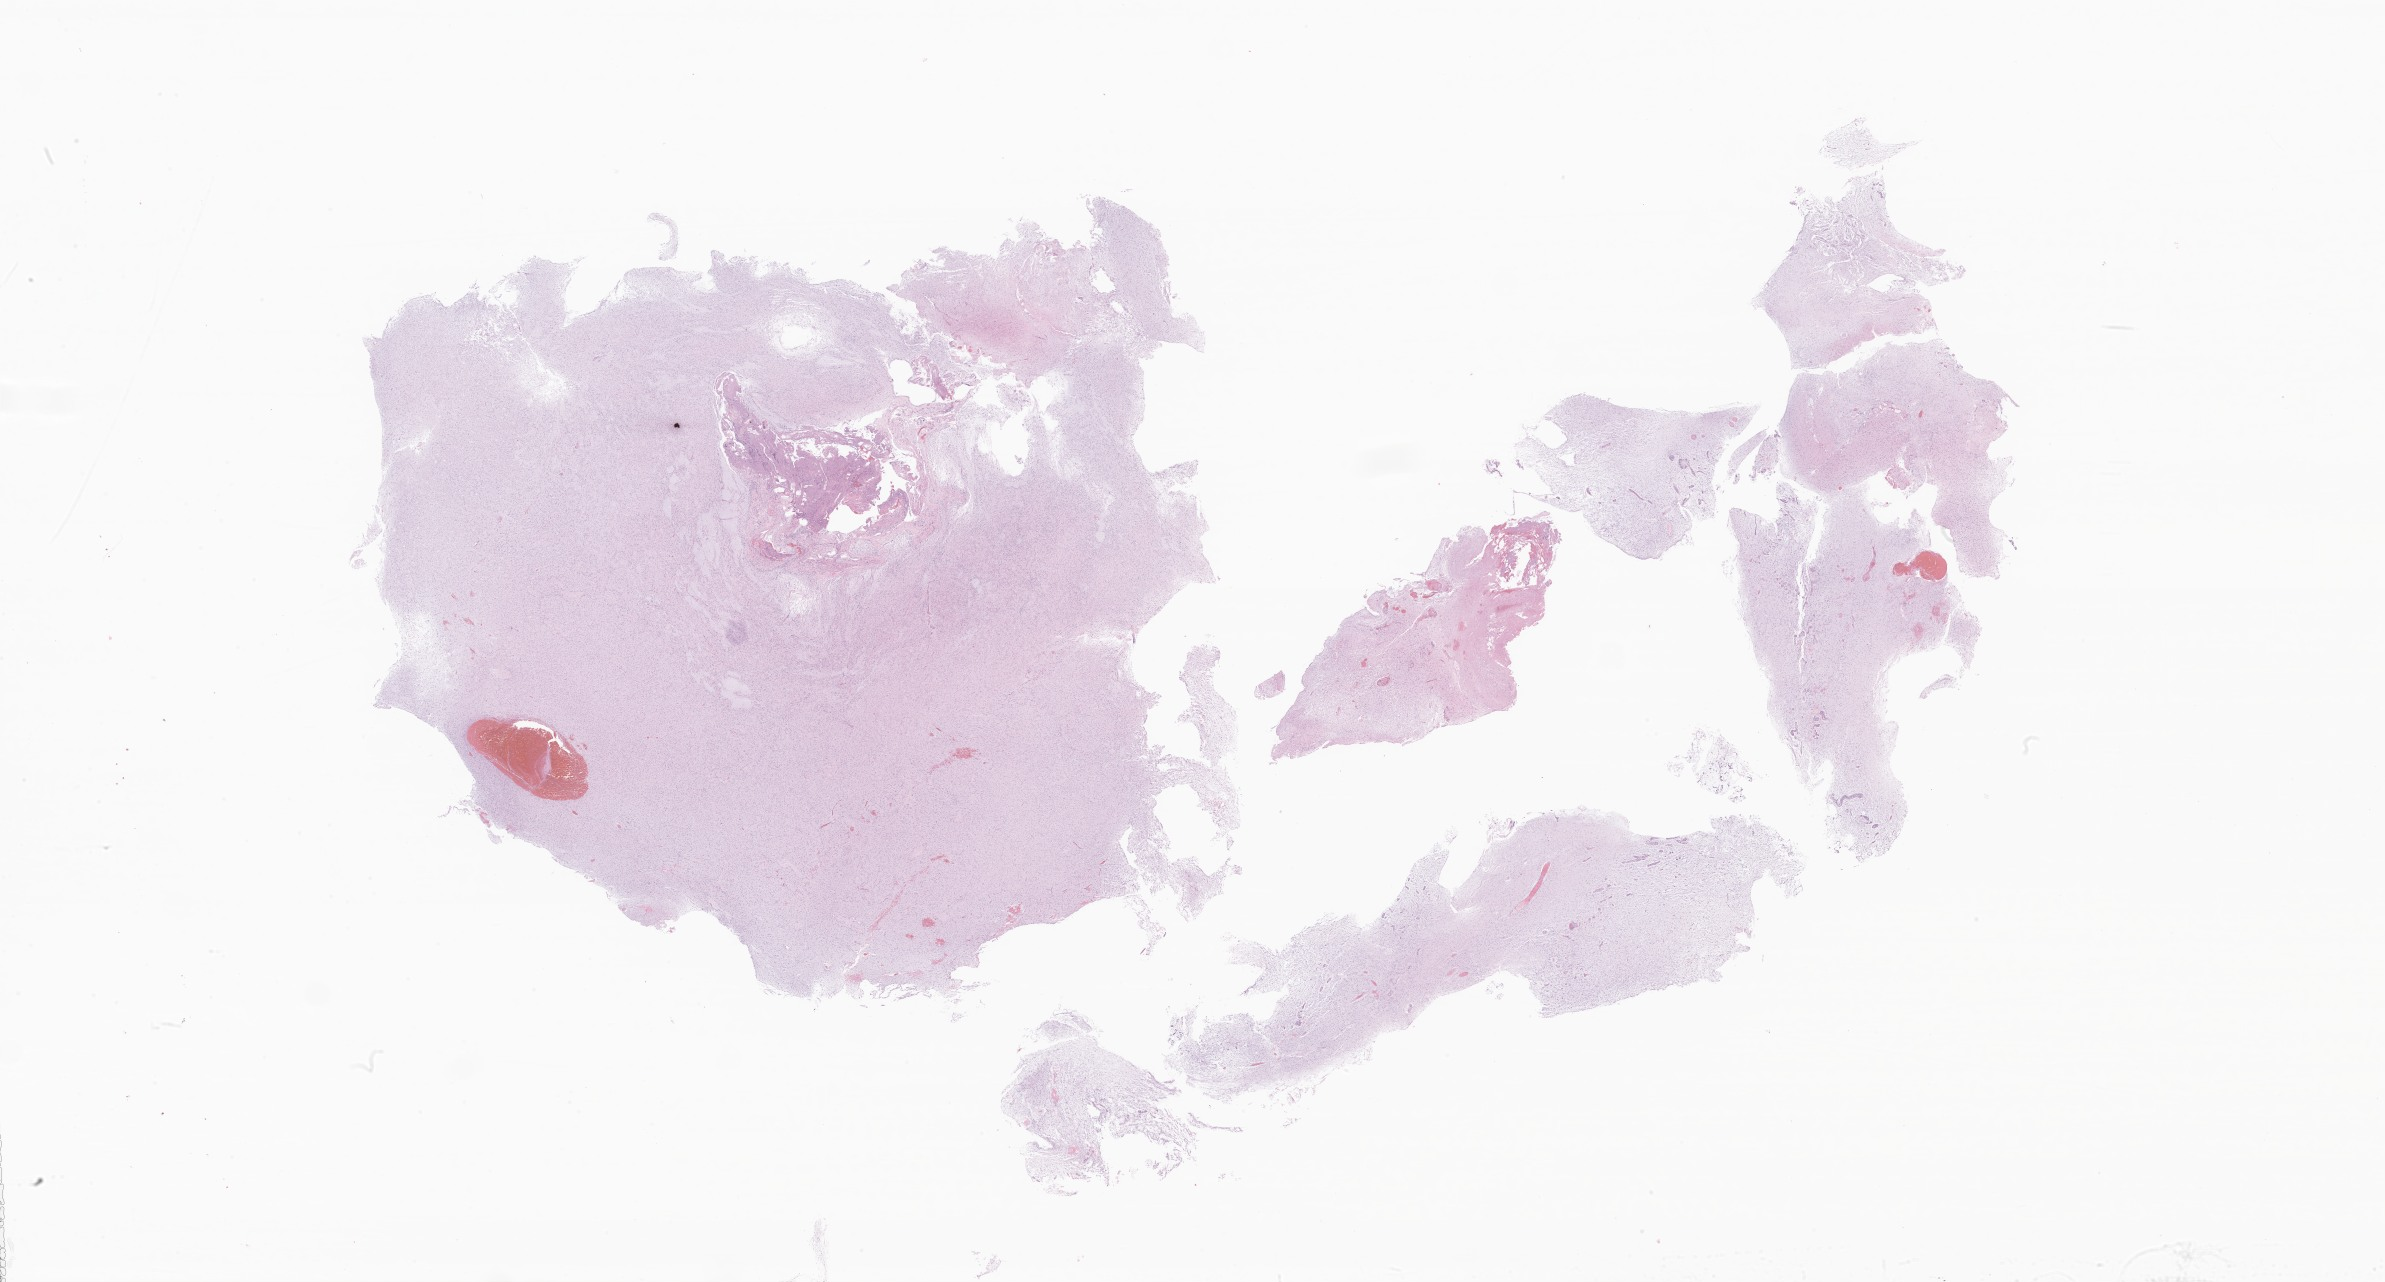
Hematoxylin and eosin (H&E) whole-slide image of tumor tissue from the brain, whole scanned area (about 40.2 x 21.6 mm) shown as a low-resolution overview; formalin-fixed paraffin-embedded section. Female patient, age 148 months.
Diagnosis: Pilocytic astrocytoma.